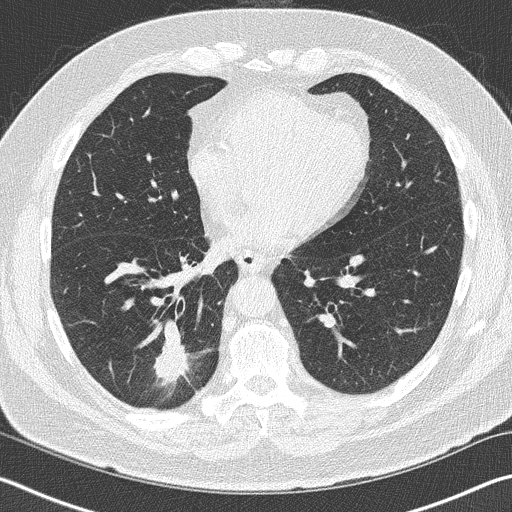
Low-dose screening chest CT, axial slice. First (baseline) screen. Lung window (W 1500 / L -600 HU). Lung (sharp) reconstruction kernel (B50f). 512 × 512 image matrix. Male, age 70 years at enrolment. Current smoker at enrolment.
Expert-annotated lung lesion, box from (x=139, y=331) to (x=213, y=402) px. Reader record for this screening exam (exam-level; its link to the box is not recorded): non-calcified nodule or mass ≥4 mm, right lower lobe, 28 × 23 mm, spiculated (stellate) margins, soft tissue attenuation.